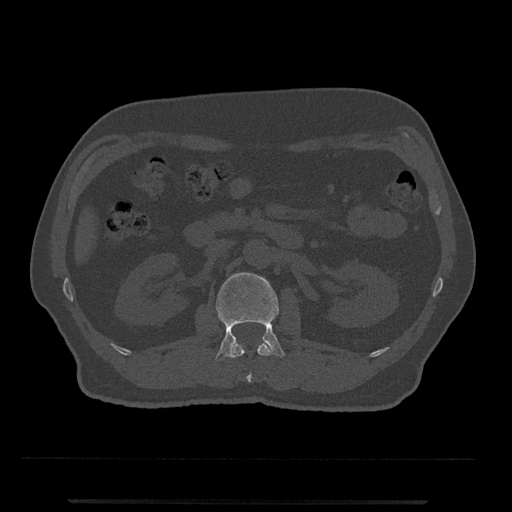
CT including the spine, one axial slice. Slice 291 of 797 in the series (ordered by position). 120 kVp. Bone window (W 1800 / L 400 HU). 0.5 mm slice thickness. 512 × 512 image matrix, field of view 419 × 419 mm. Patient: male, 63 years. From the clinical record (not read from this slice): primary cancer: prostate.
Annotated regions visible in this slice (semi-automatic segmentation, software-assisted and operator-edited):
- L1 vertebra: bounding box [x1, y1, x2, y2] px = [229, 342, 273, 382]
- L2 vertebra: [215, 272, 285, 361]